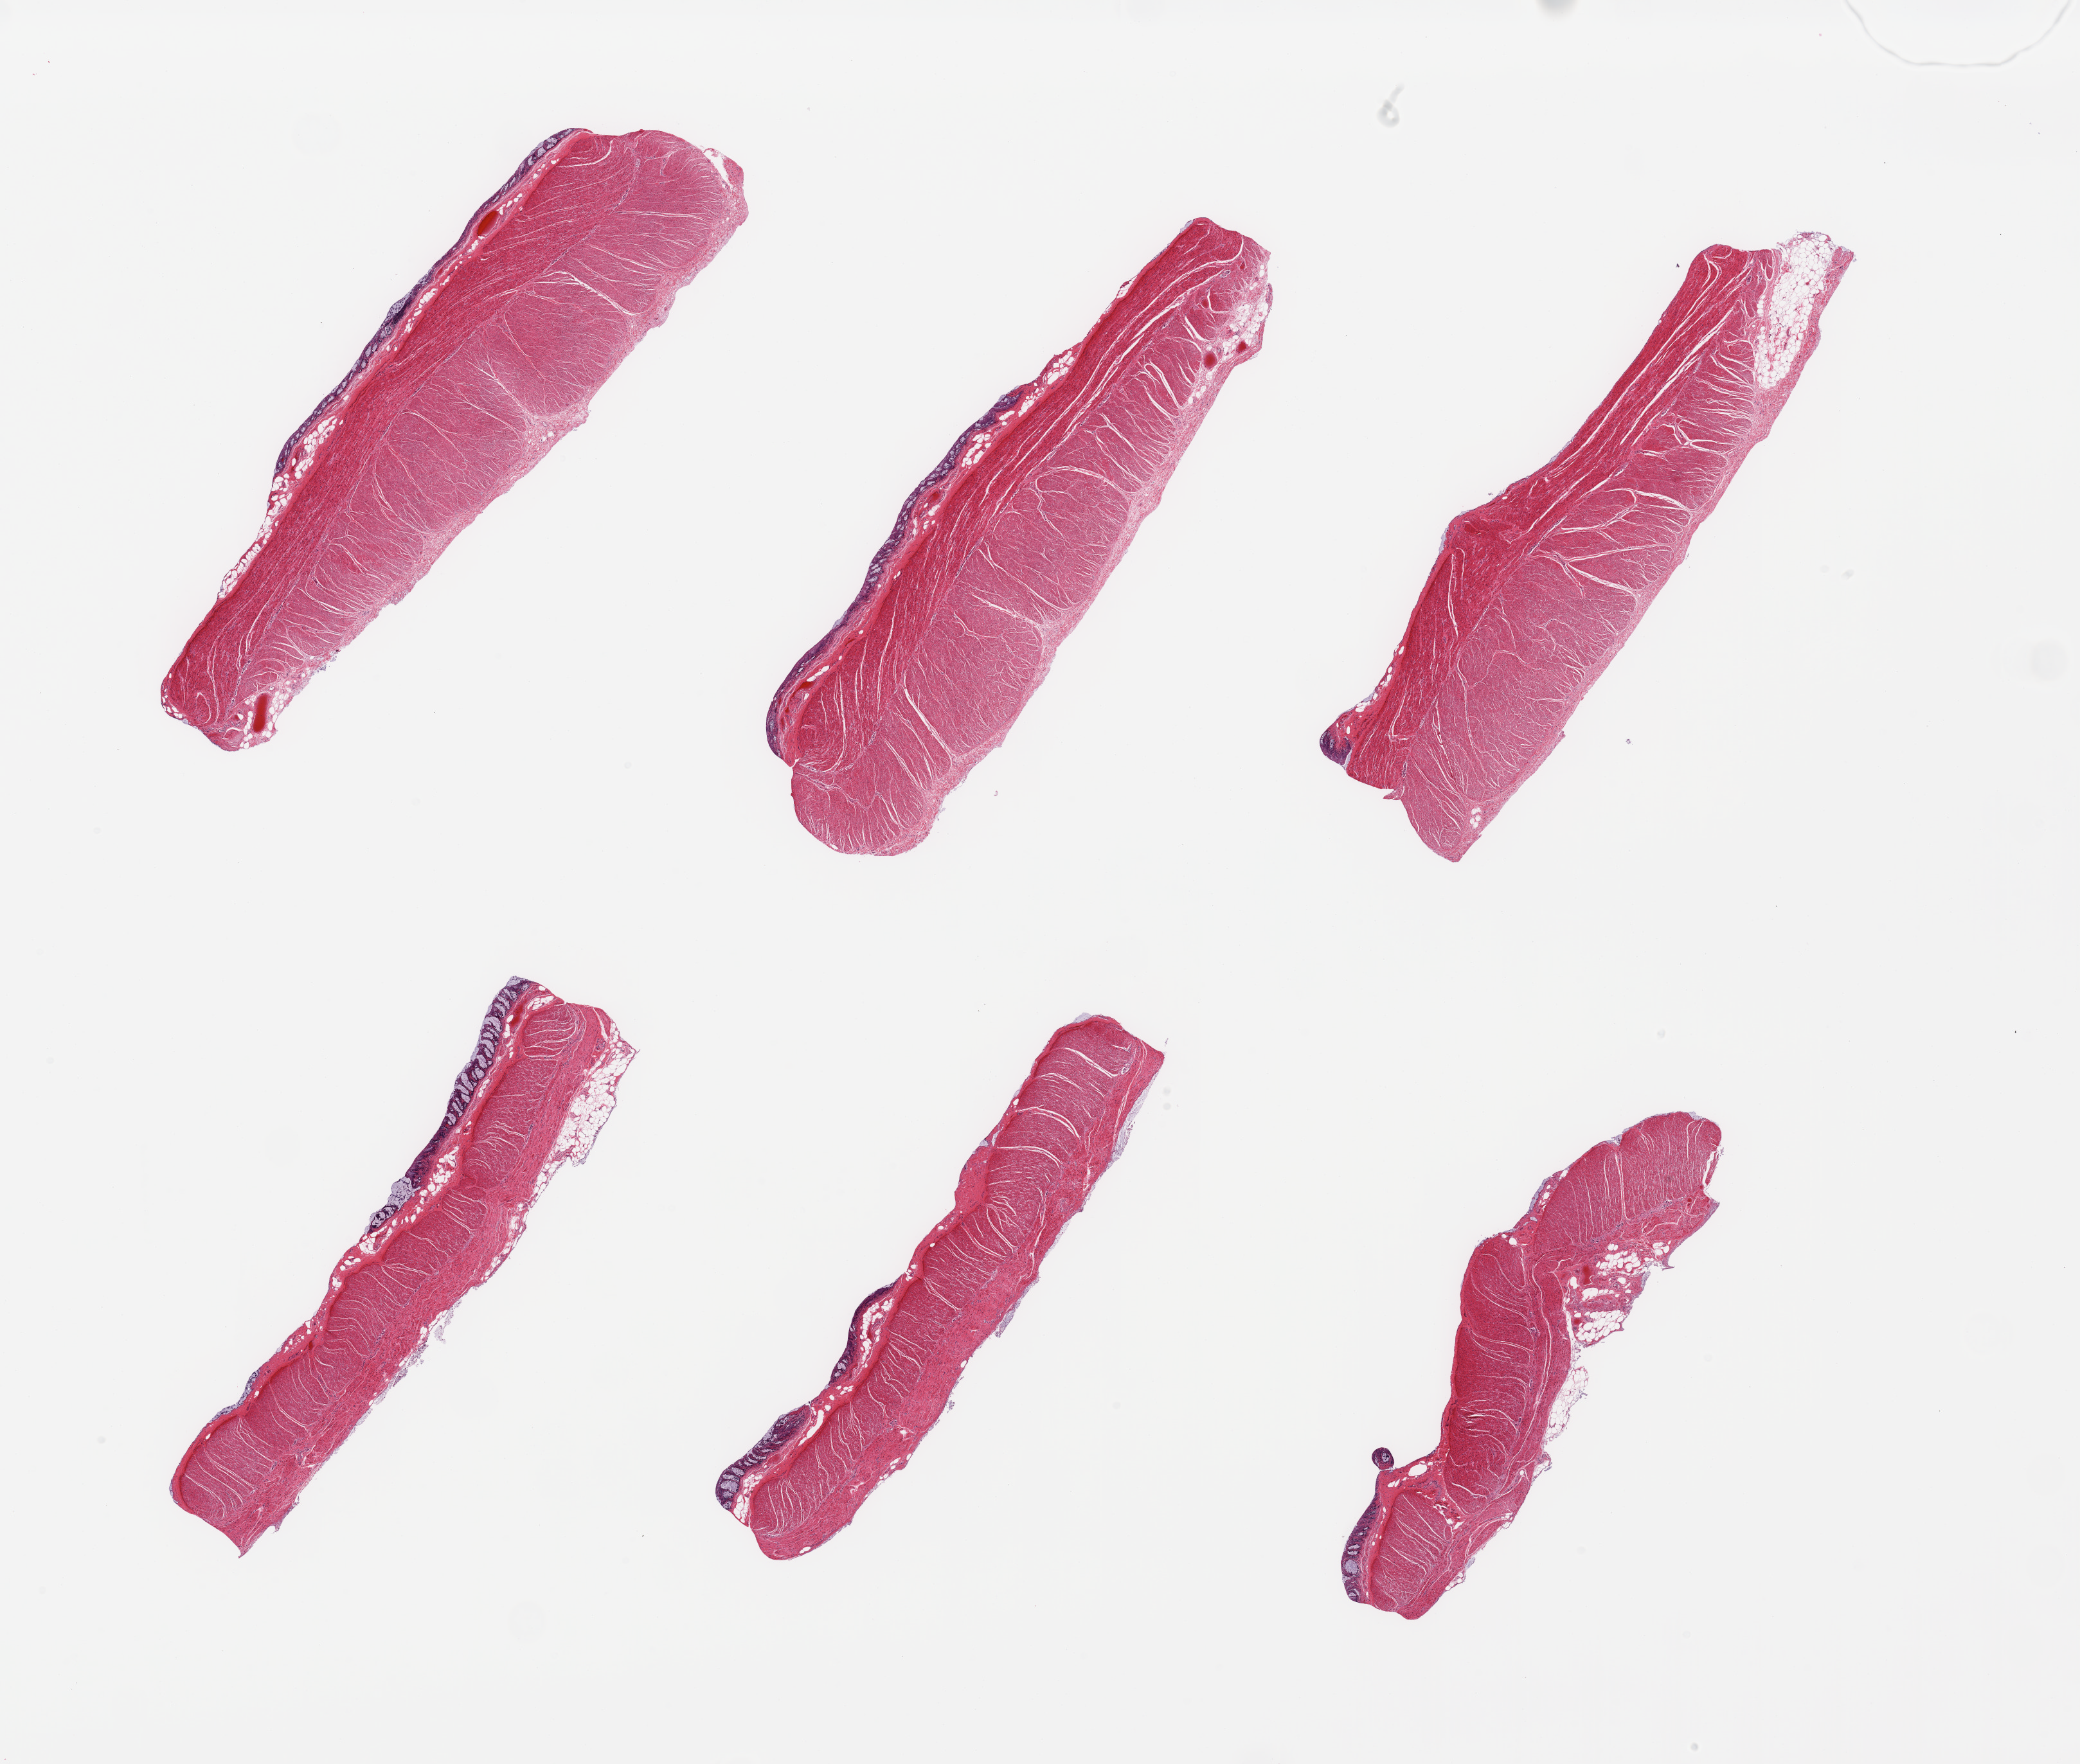
Digitized H&E-stained section, whole scanned area (about 25.6 x 21.7 mm) shown as a low-resolution overview. PAXgene-fixed, paraffin-embedded tissue. Target tissue: sigmoid colon. Tissue donor sample.
Reviewer comment on this tissue sample: 6 pieces; thin remnants of mucosa on all; questionable value.